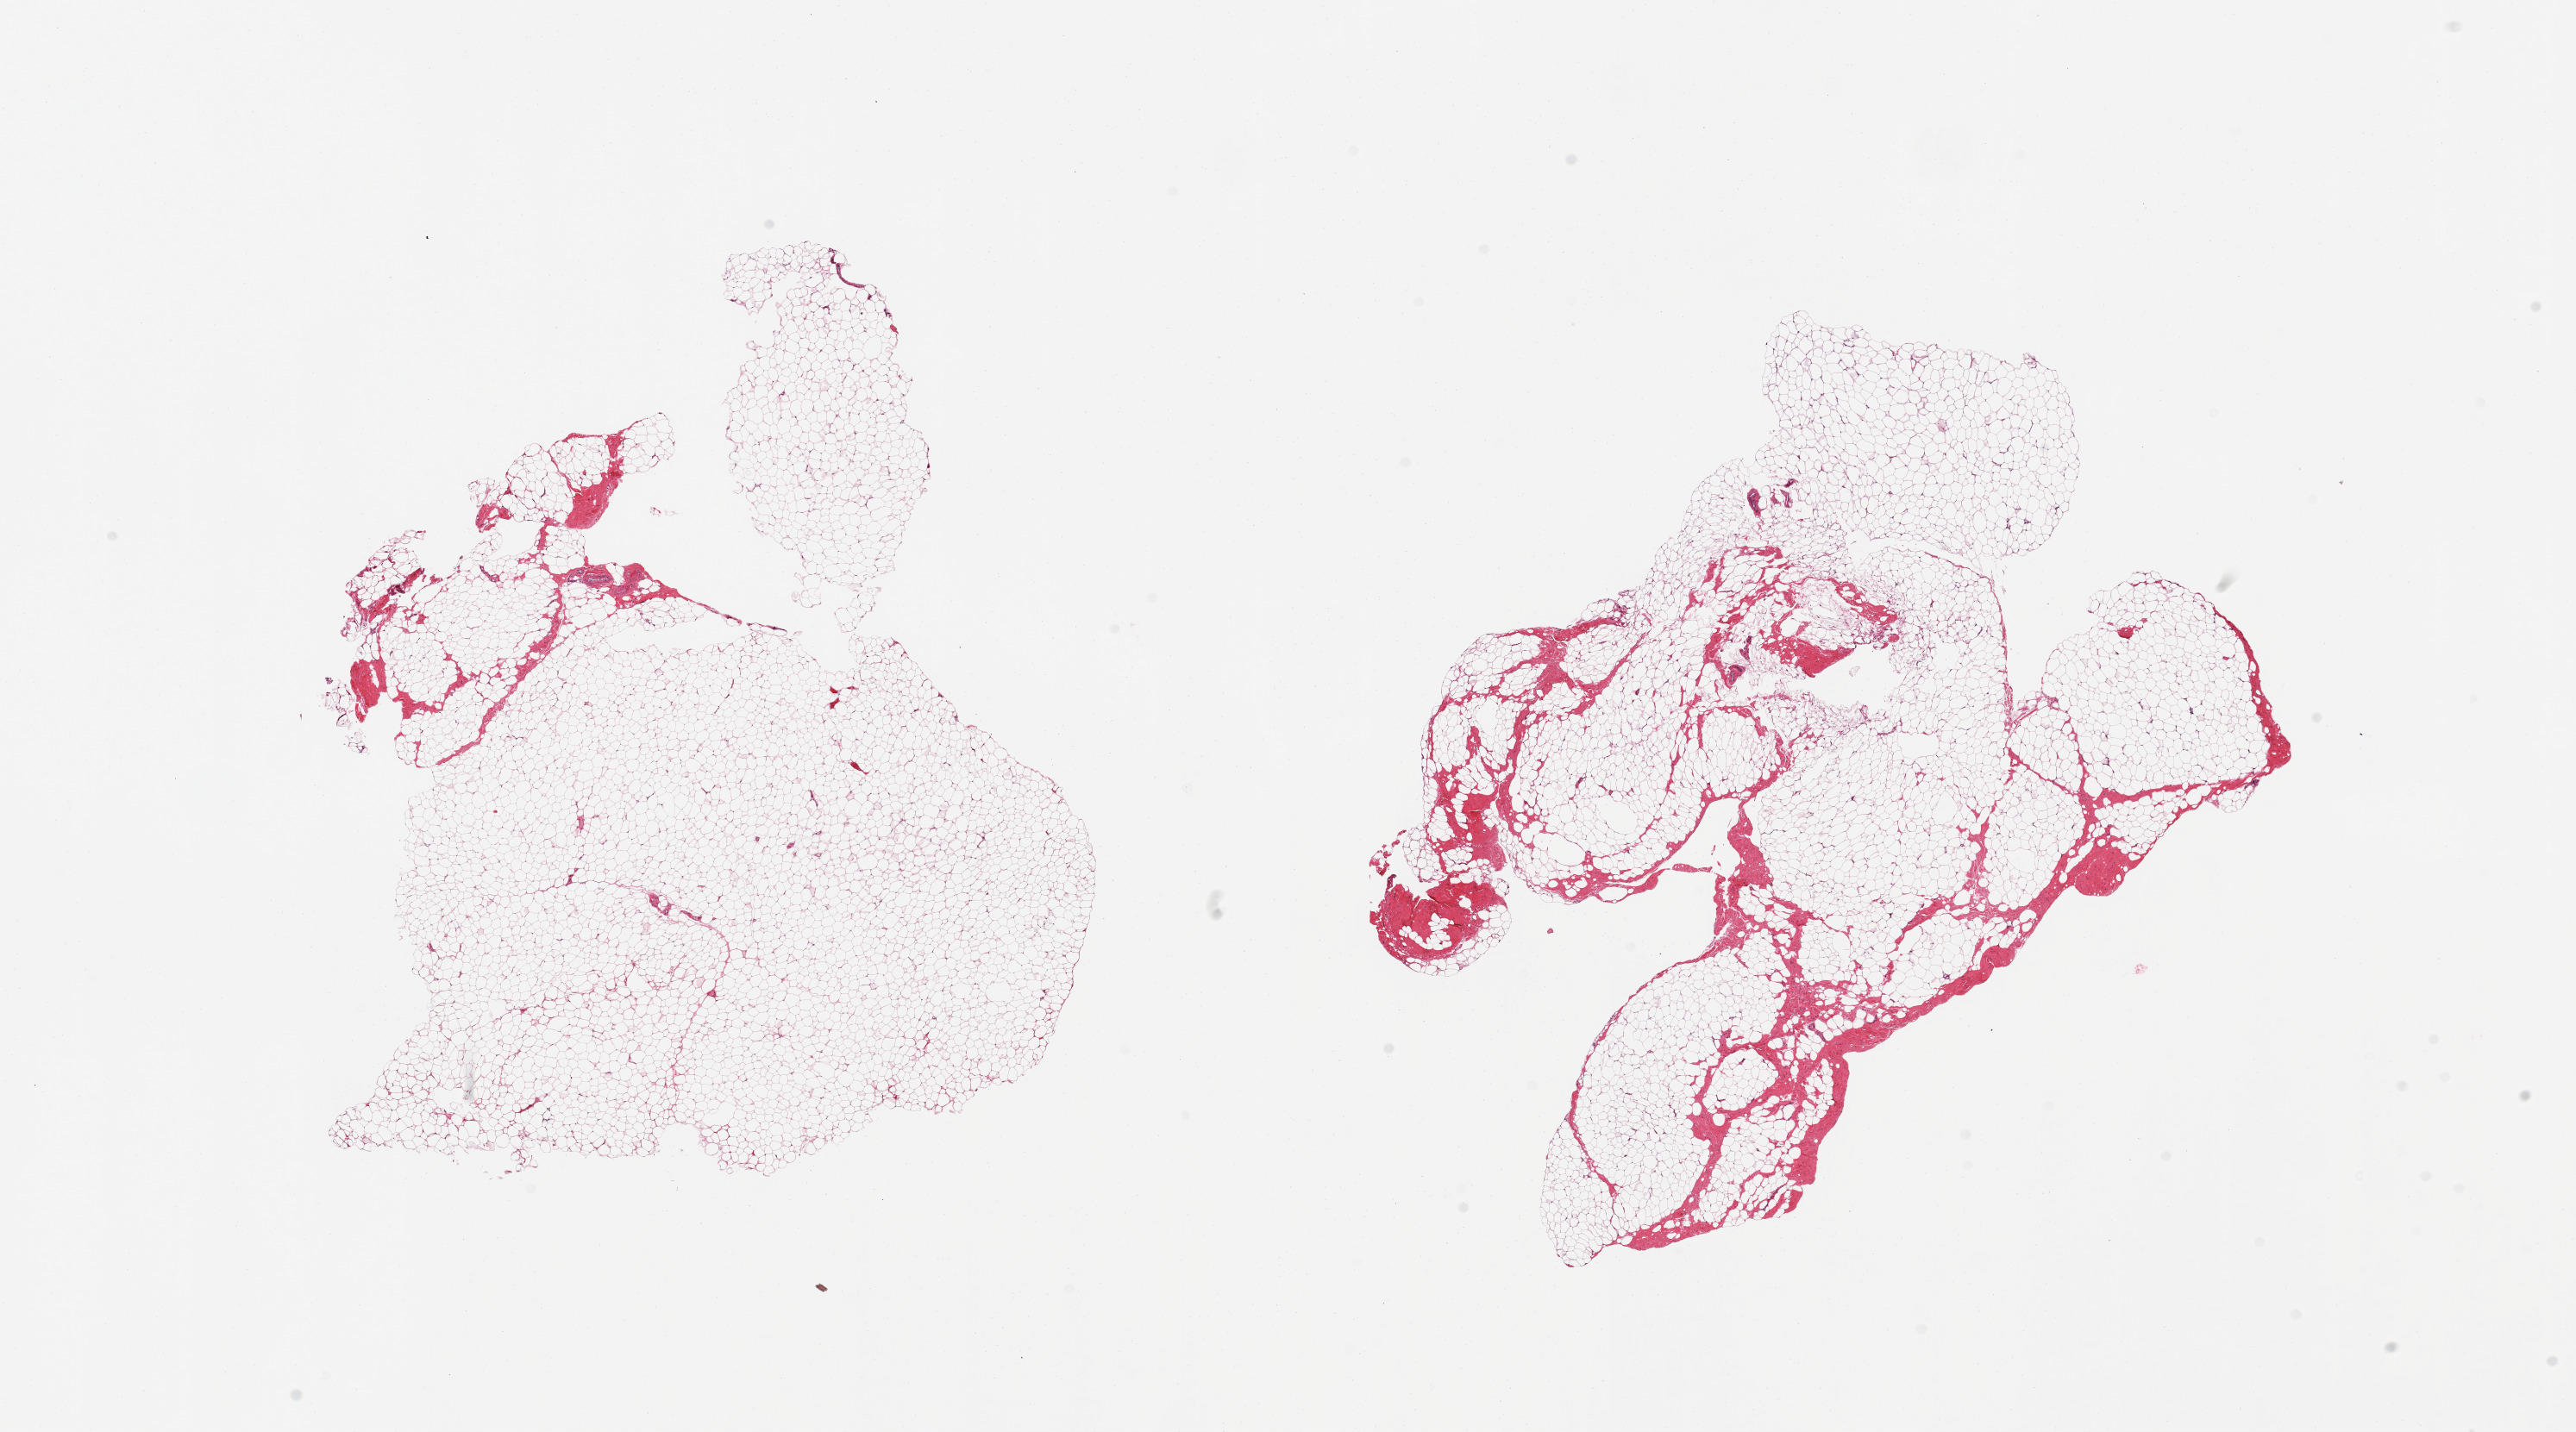
Whole-slide image, hematoxylin and eosin (H&E) stain, a low-resolution overview of the entire scanned area, about 23.6 x 13.1 mm, PAXgene-fixed paraffin-embedded (PFPE) section, target tissue: breast, tissue donor sample. Donor: male.
• pathologist's review note for this sample: 2 pieces; no ducts; 5% fibrous content